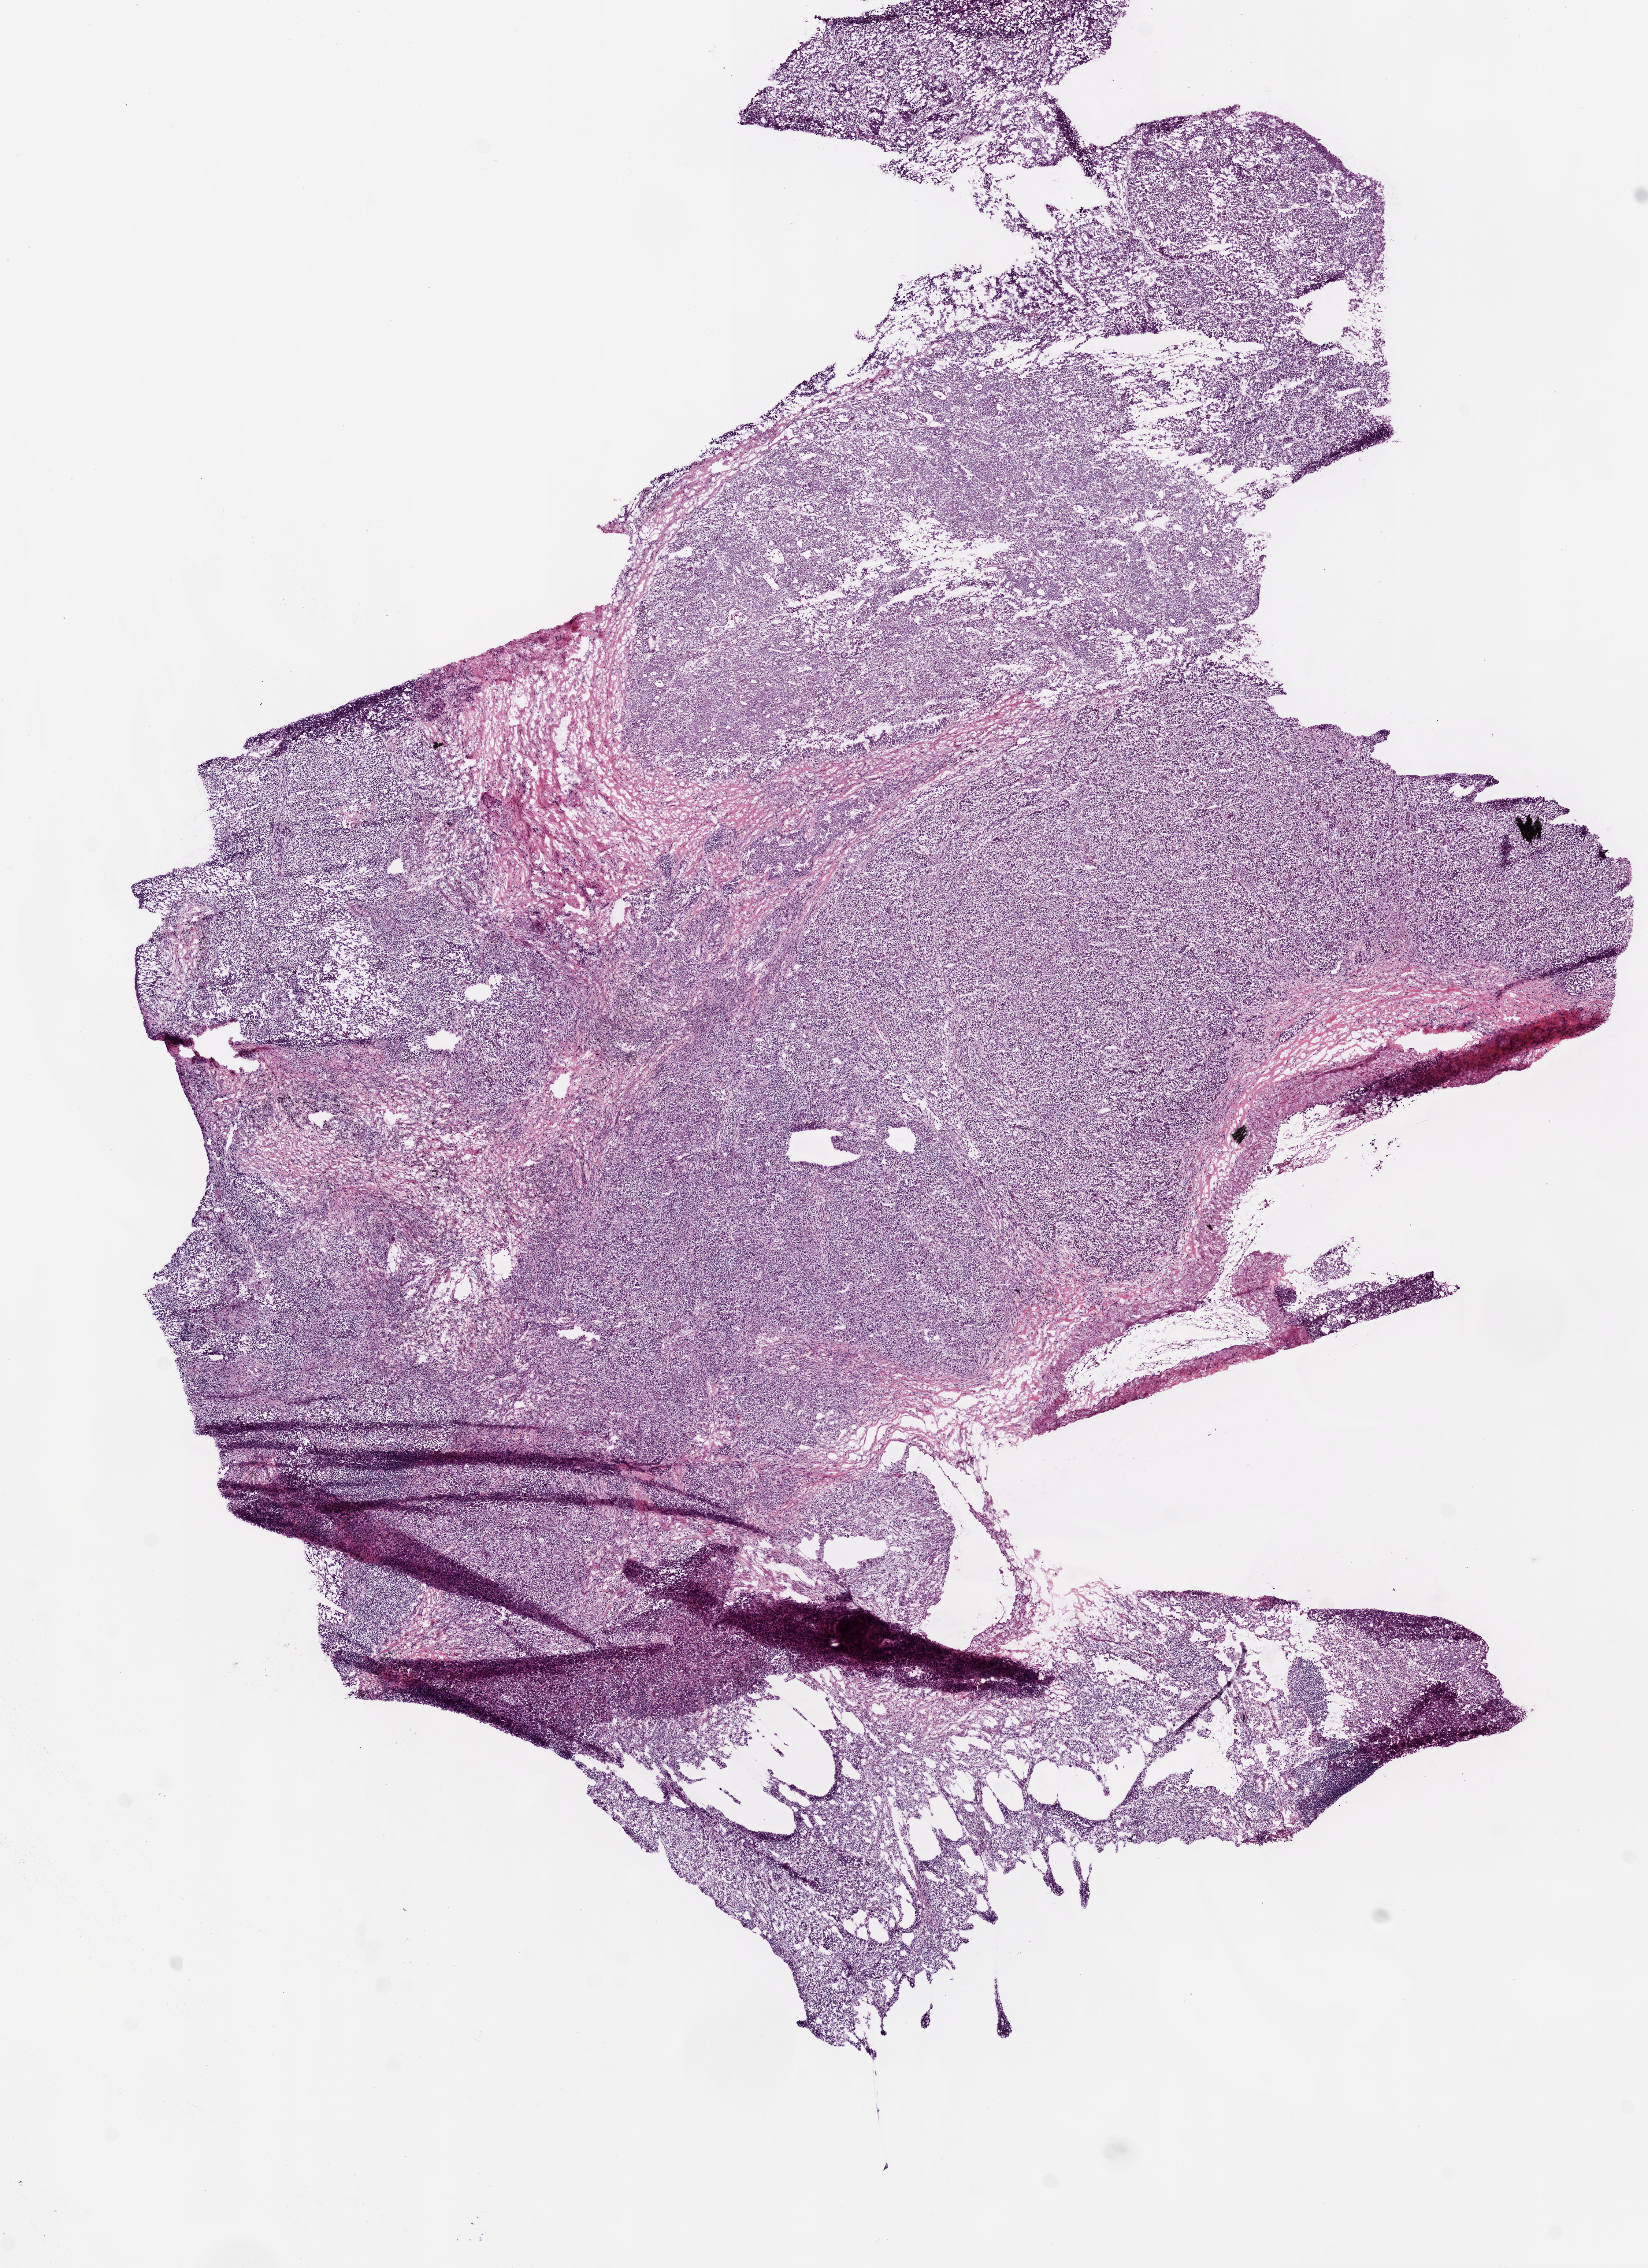
H&E-stained whole-slide image, whole scanned area (about 9.0 x 12.4 mm, slide scanned at 20x) shown as a low-resolution overview, frozen section from the top of the tissue portion, sample: primary tumour, lung. Patient: male, age at initial diagnosis 70 years. Slide review estimates, as recorded: tumour cells 82%, tumour nuclei 75%, normal cells 0%, stromal cells 15%, necrosis 3%.
Diagnosis: Adenocarcinoma with mixed subtypes (upper lobe, lung). AJCC pathologic stage: IA (5th edition).